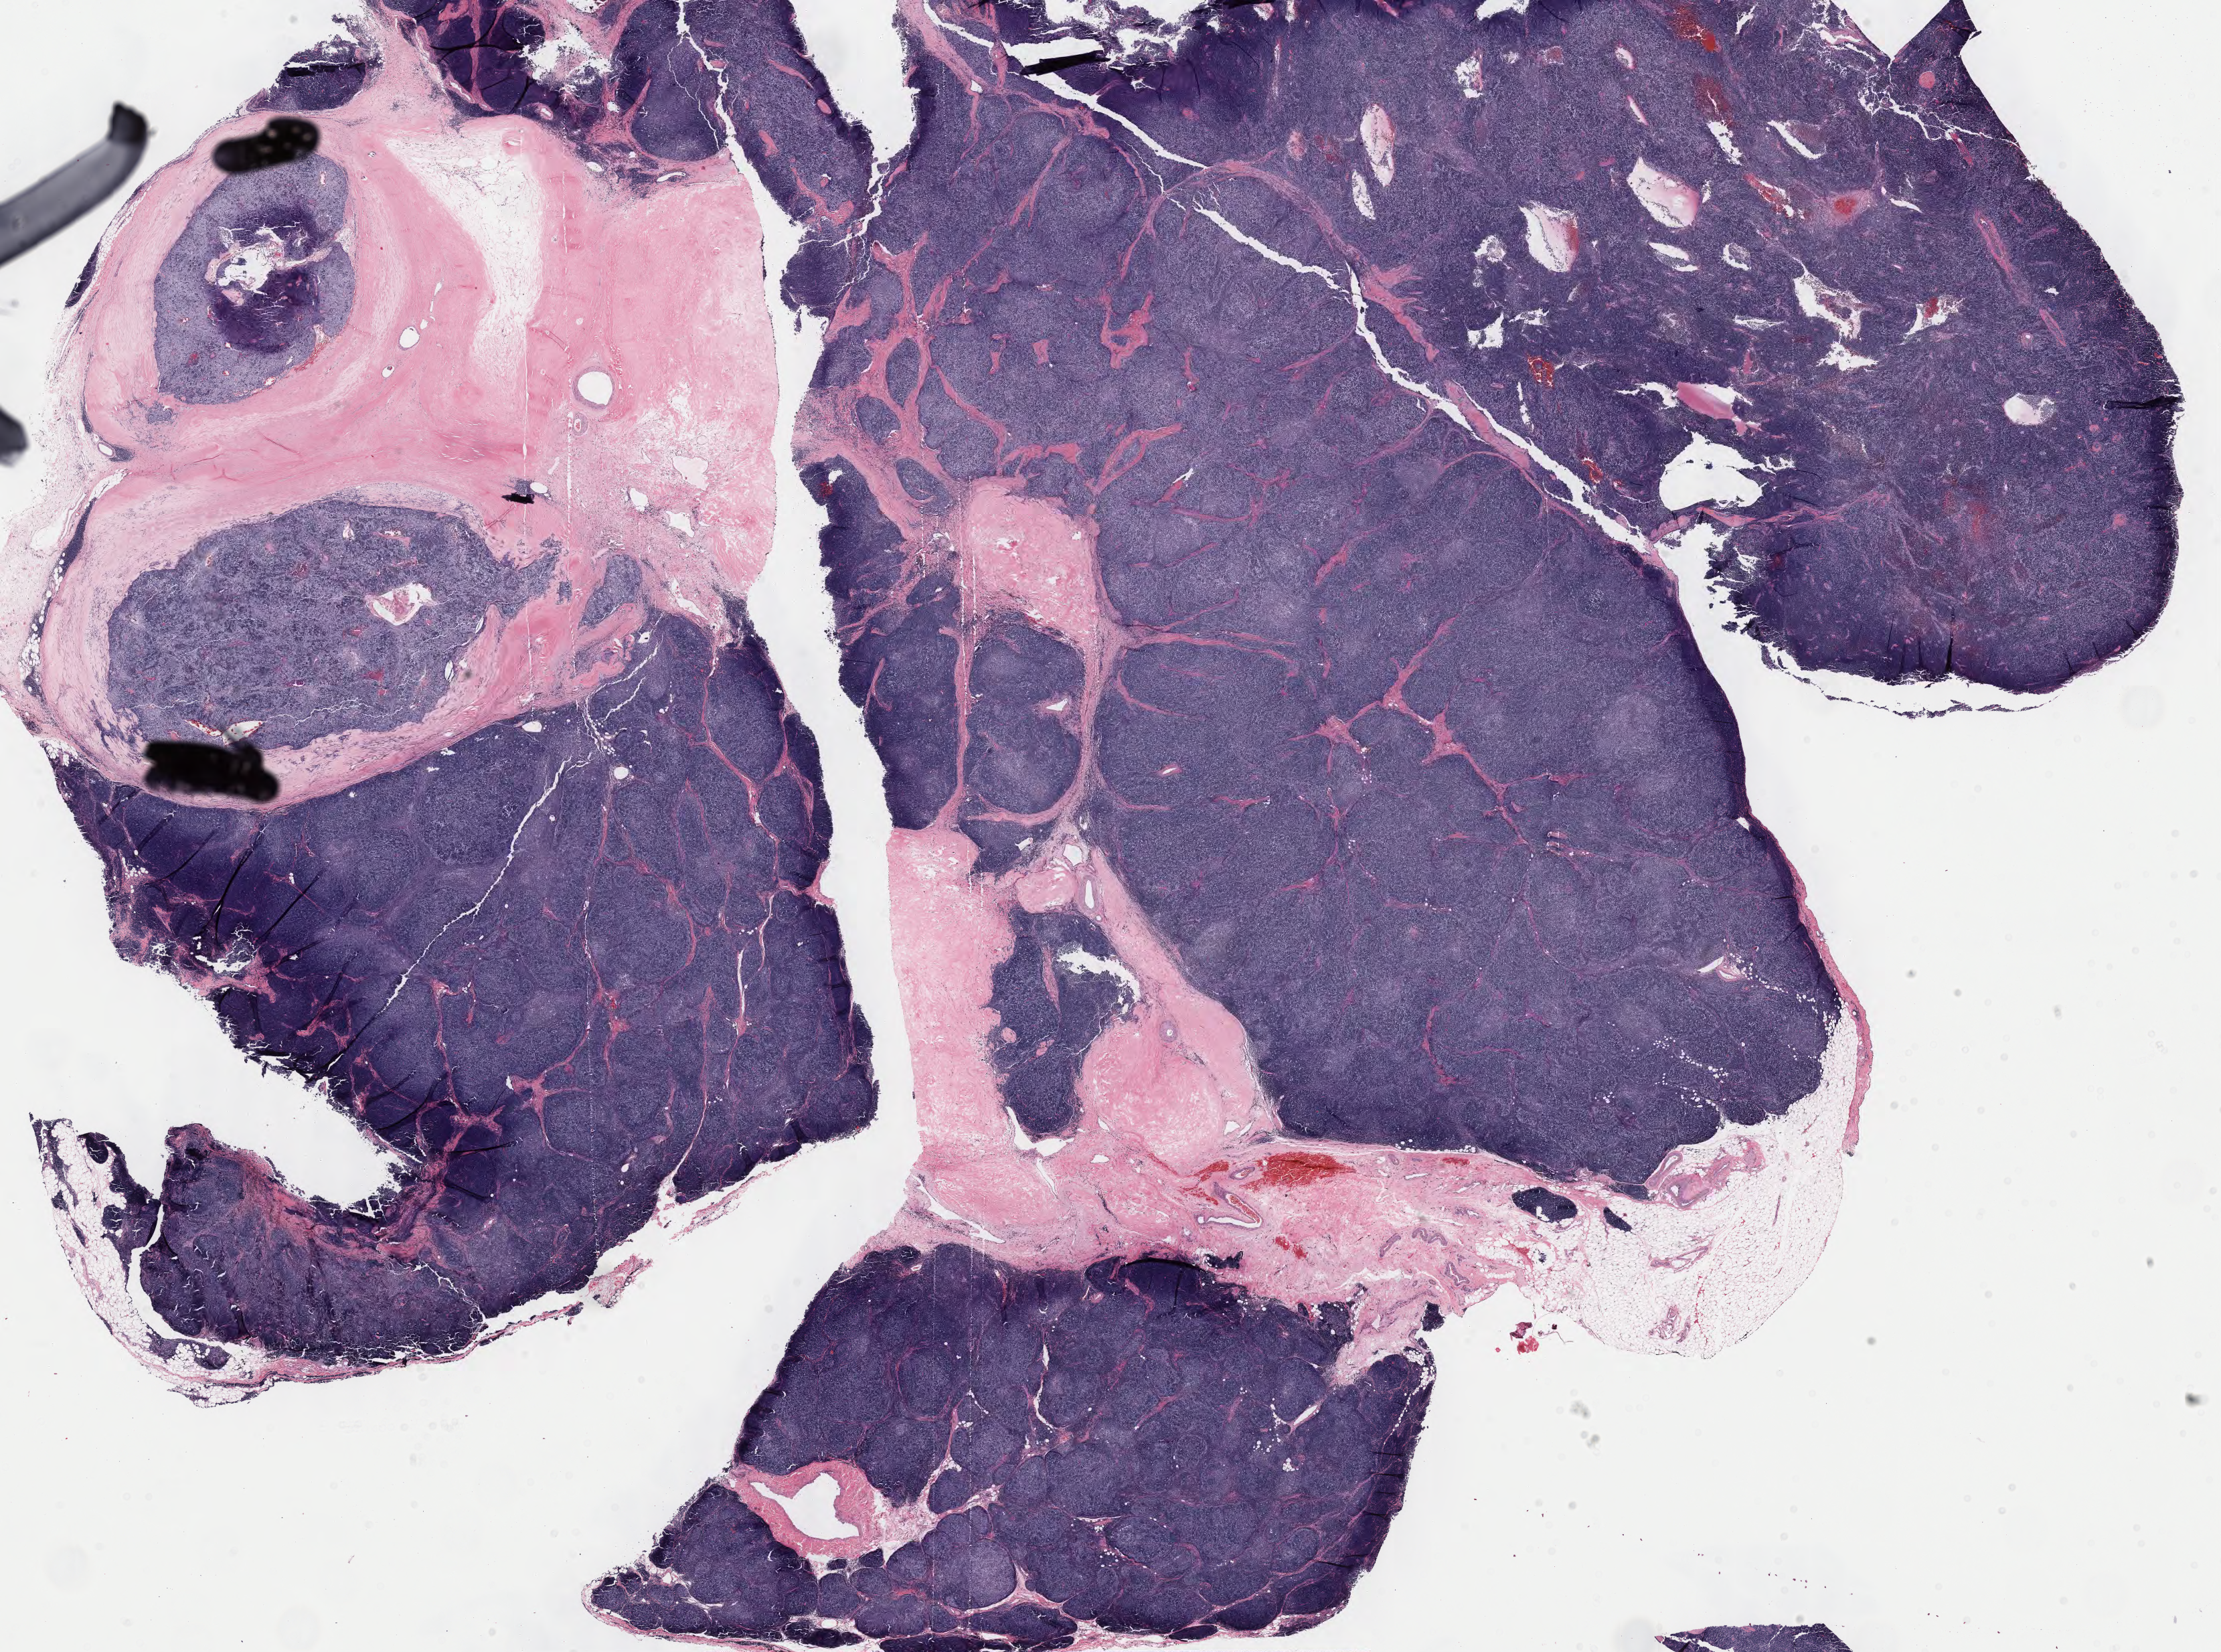
Digitized Hematoxylin and eosin (H&E) stained tissue section (whole slide) — whole scanned area (about 26.3 x 19.6 mm, from a 40x scan) shown as a low-resolution overview, formalin-fixed paraffin-embedded (FFPE) diagnostic section, primary tumour sample from the thymus. Male patient; age at initial diagnosis 44 years.
Histologic diagnosis: Thymoma, type B2, malignant.